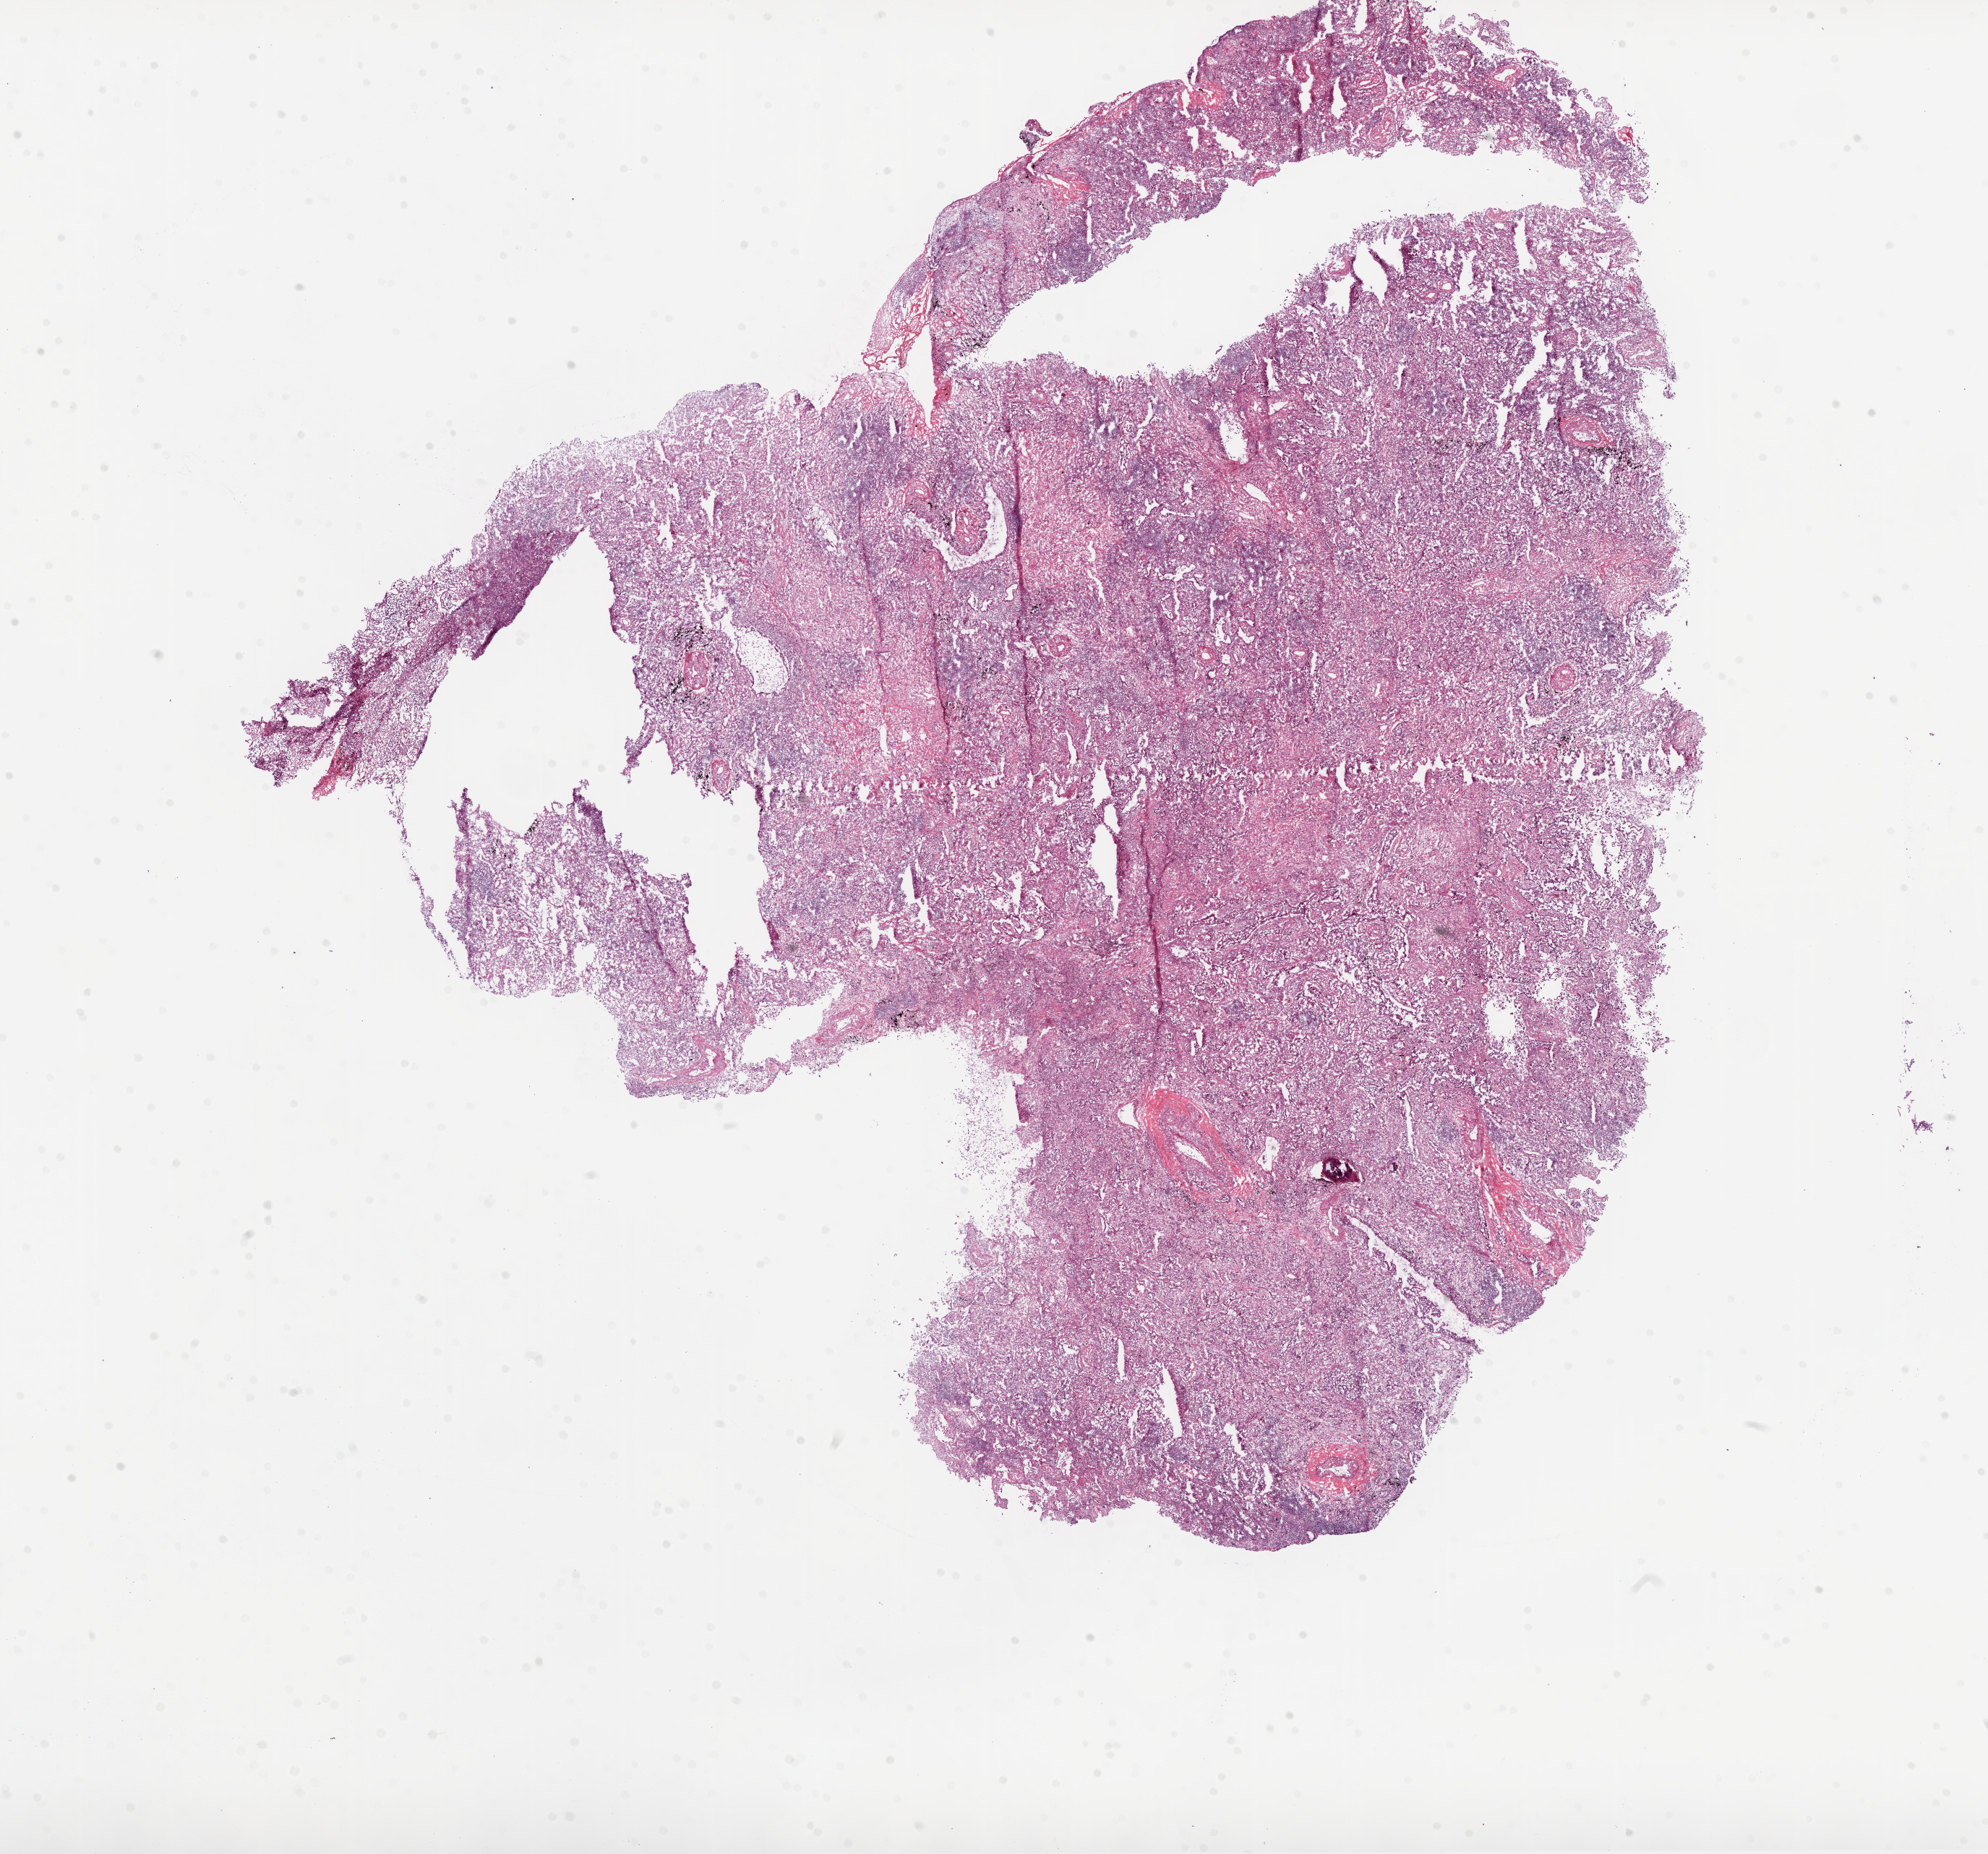
Whole-slide histology image, H&E-stained, whole scanned area (about 22.1 x 20.6 mm, acquisition: 20x scan) shown as a low-resolution overview, frozen section from the top of the tissue portion, lung, primary tumour sample. Patient: female, age at initial diagnosis 79 years. Composition of this section per pathologist review: tumour cells 65%, tumour nuclei 60%, normal cells 20%, stromal cells 15%, necrosis 0%.
AJCC pathologic stage: IIA (6th edition). Histologic diagnosis: Adenocarcinoma with mixed subtypes.